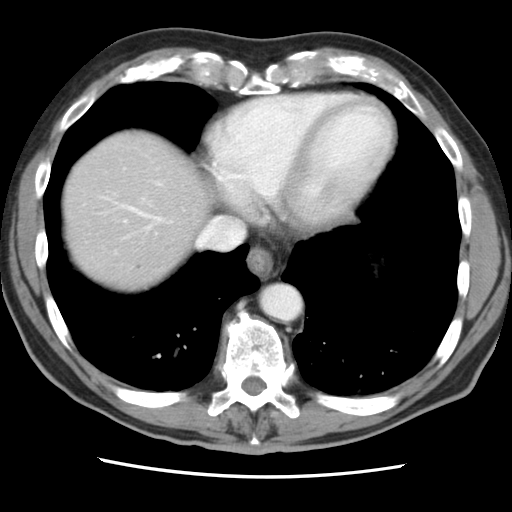
Contrast-enhanced abdominal CT, one axial slice. Position 77 of 83 along the scan axis. 120 kVp. Soft-tissue window (W 400 / L 40 HU). 5 mm slice thickness. 512 × 512 image matrix, field of view 321 × 321 mm. Male patient, age 69 years. Case-level facts recorded for this patient, not image findings: diagnosis: colorectal cancer liver metastases, imaged before liver resection; multiple liver metastases: yes; largest metastasis: 3.5 cm; disease in both lobes: no.
Outlined on this slice (outlined manually by an expert reader):
- hepatic veins: box from (x=119, y=204) to (x=244, y=249) px
- liver: (x=63, y=129)–(x=211, y=291)
- planned liver remnant (the part of the liver to remain after resection): (x=64, y=154)–(x=208, y=291)